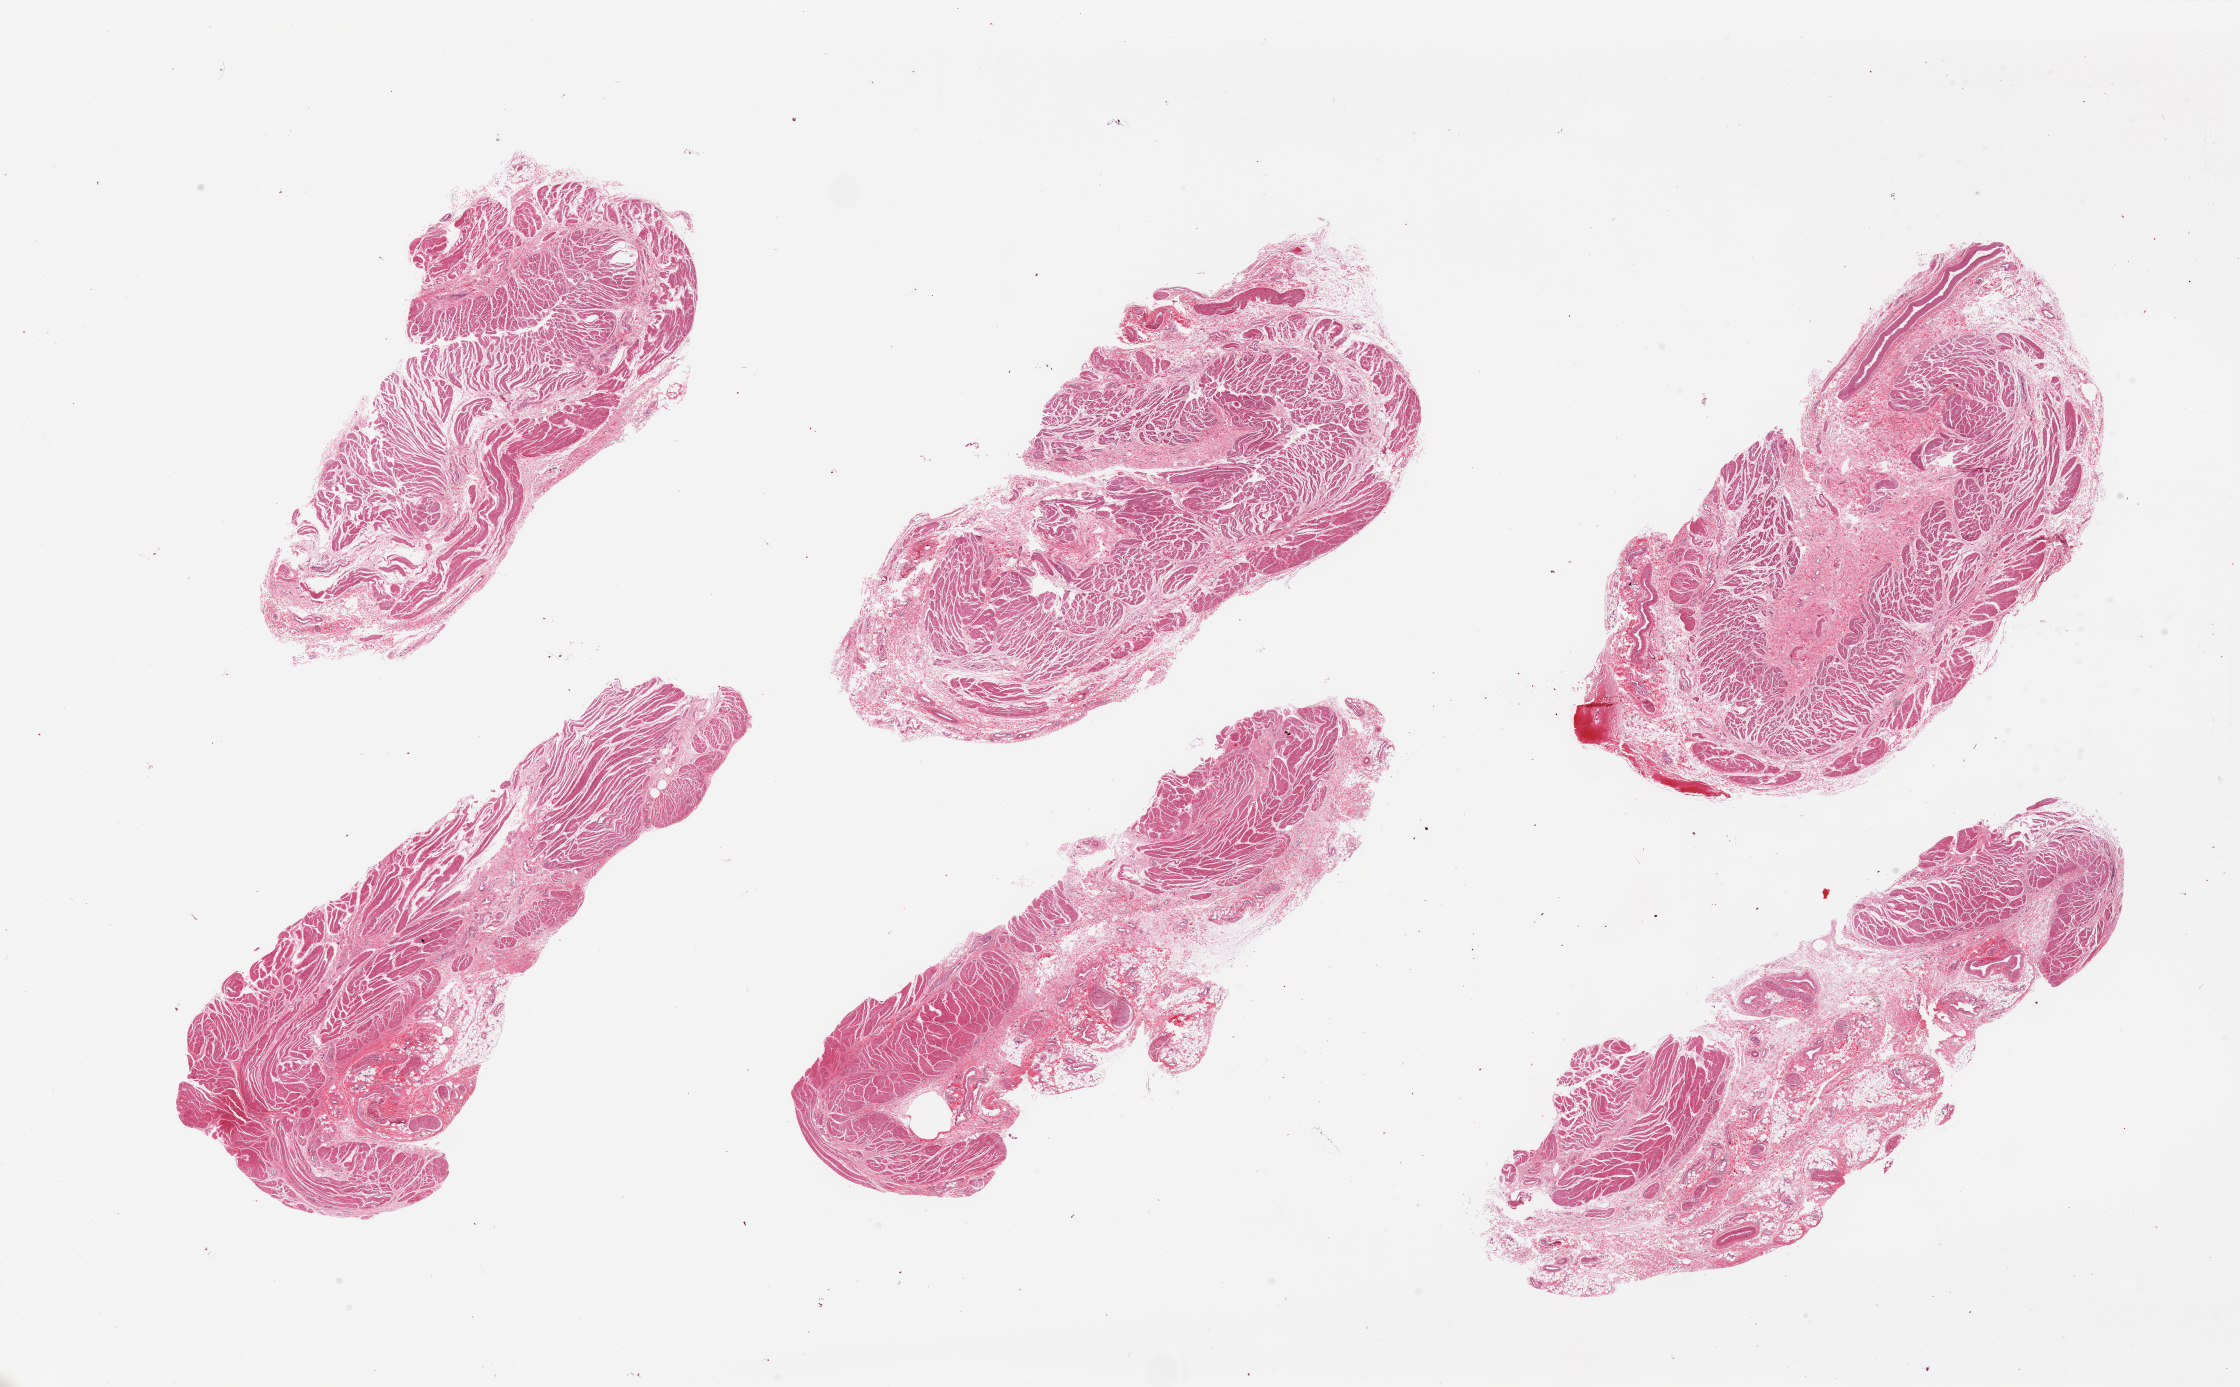
Whole-slide image, haematoxylin and eosin stain — shown as a low-resolution overview of the whole scanned area (about 35.4 x 21.9 mm). PAXgene-fixed paraffin-embedded (PFPE) section. Target tissue: gastroesophageal junction. Tissue donor sample. Donor sex: female.
- reviewer comment on this tissue sample: 6 pieces